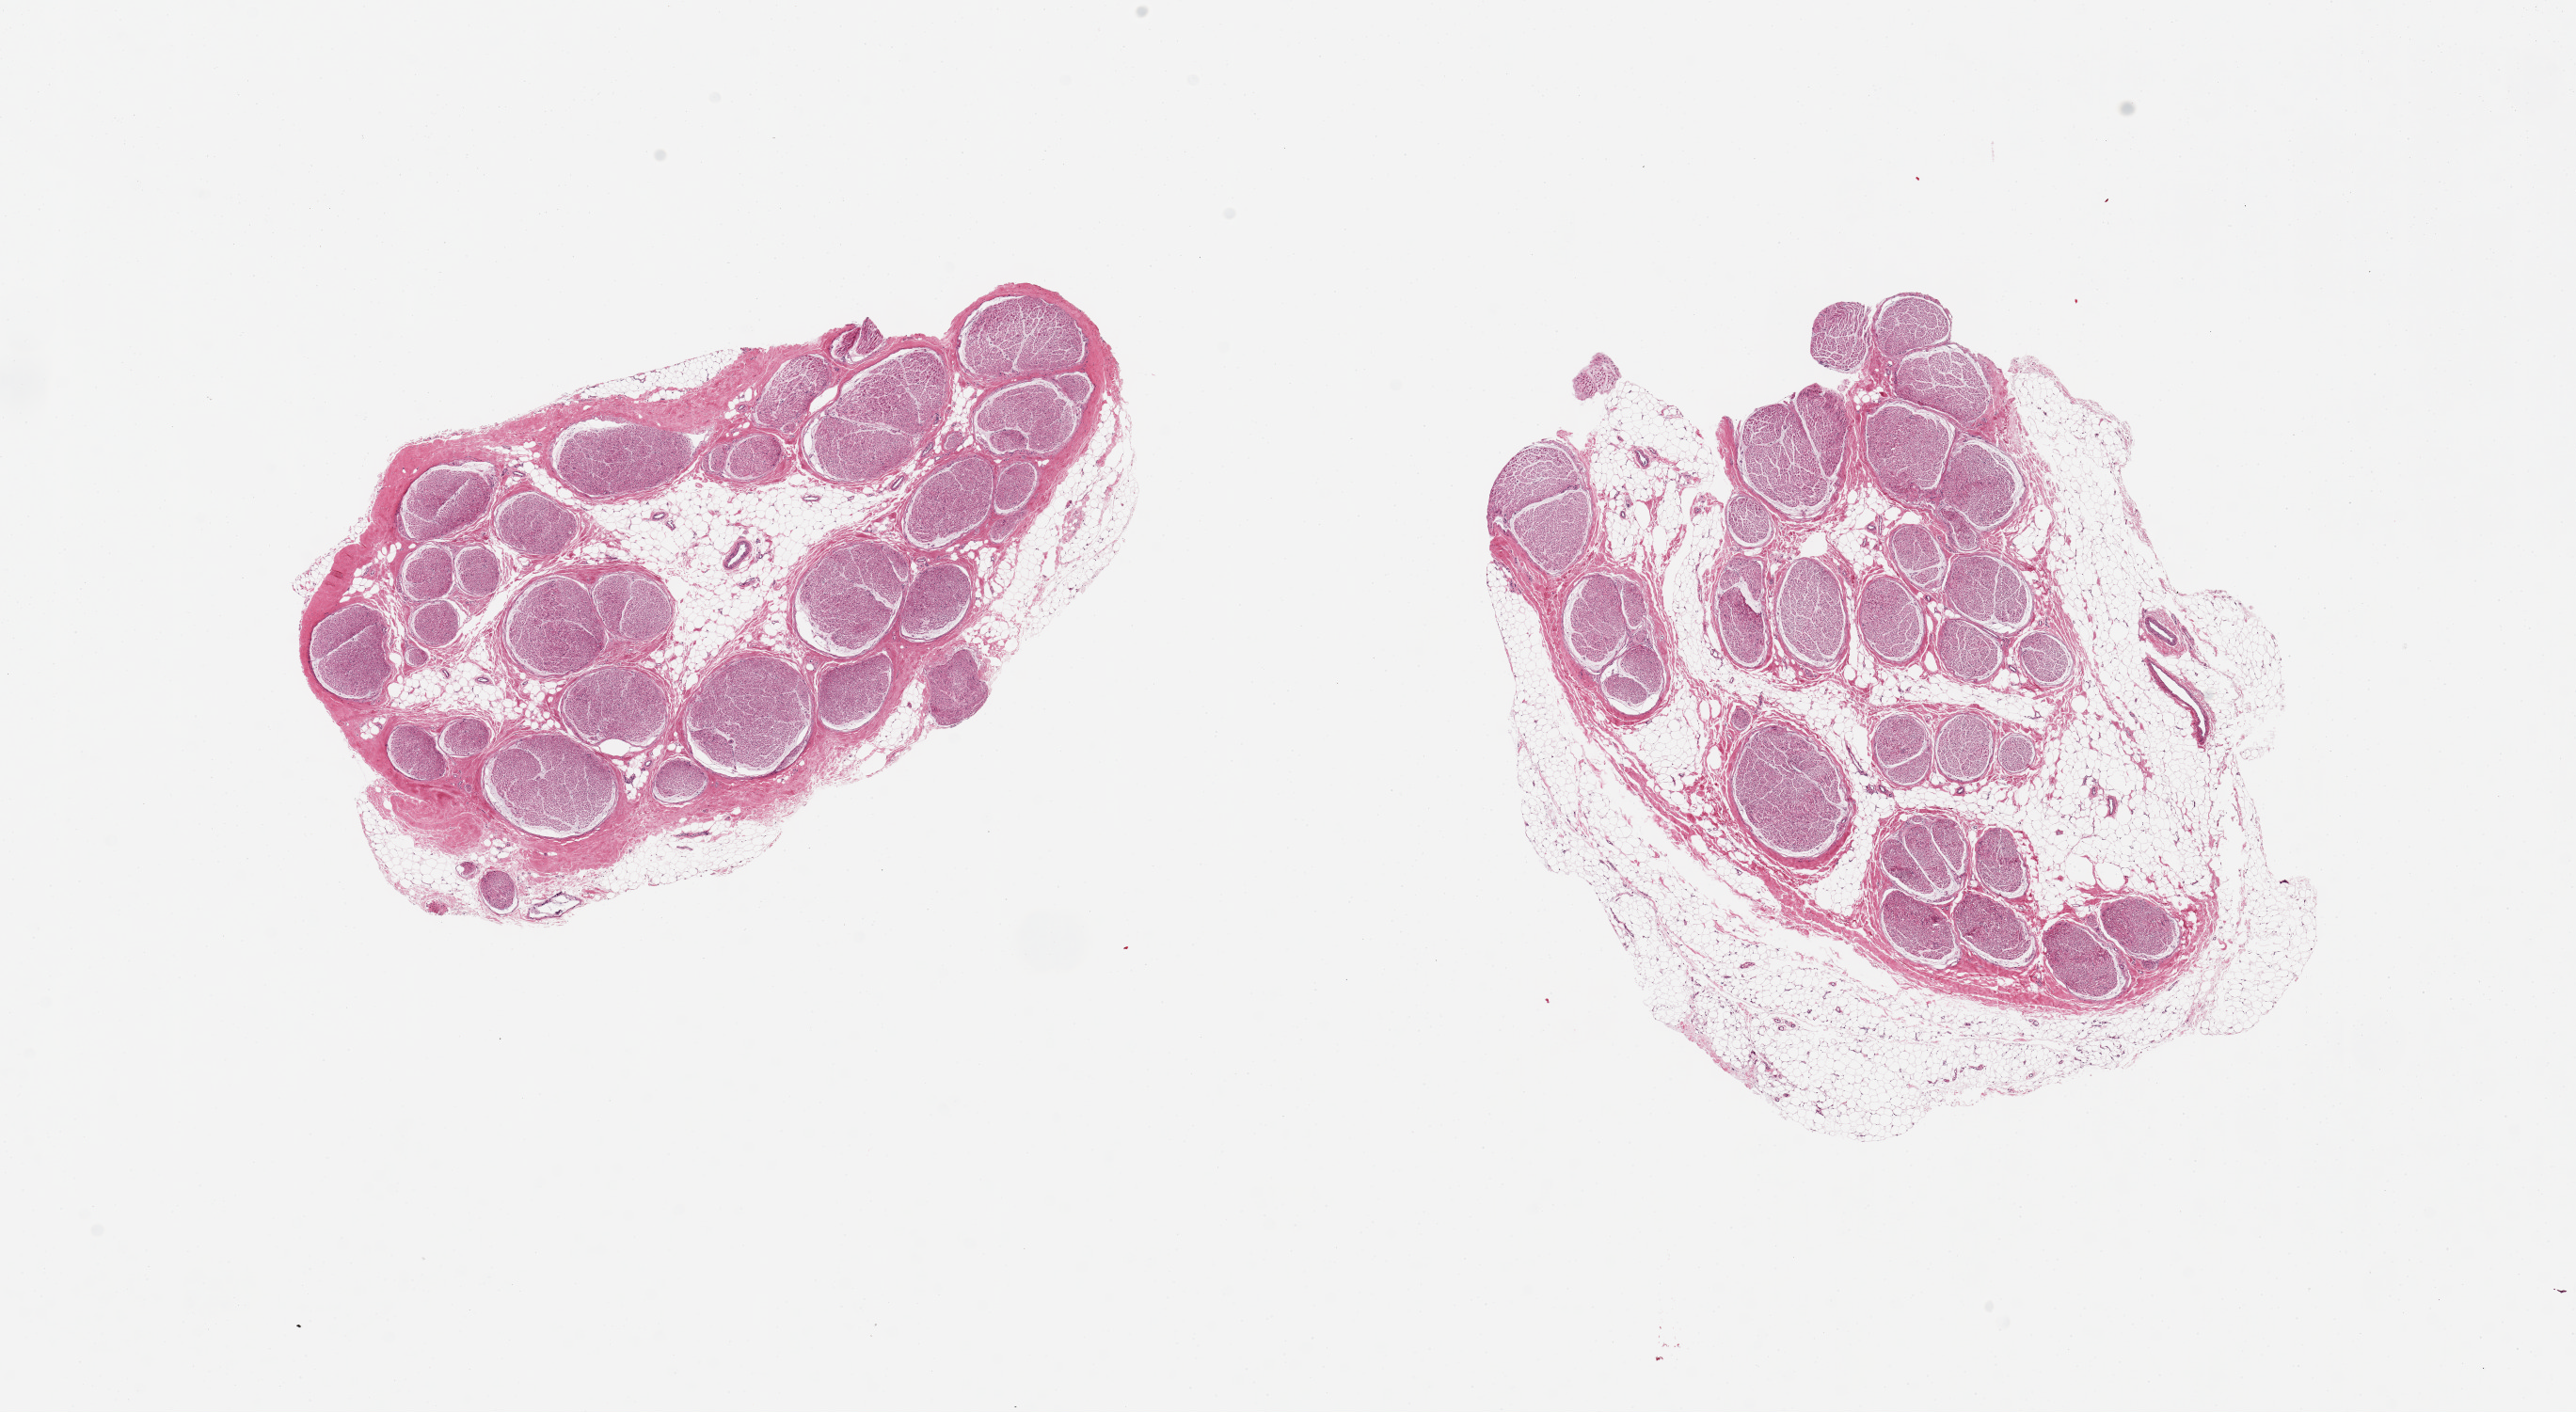
Haematoxylin and eosin whole-slide image, brightfield, low-resolution overview of the scanned area, about 21.7 x 11.9 mm; PAXgene-fixed paraffin-embedded (PFPE) section; sampled site (target tissue): tibial nerve; tissue donor sample. Donor: female.
* pathologist's review note for this sample: 2 pieces, 7.5x5 & 8x6mm; ~1-15.mm rim of discontinuous flat